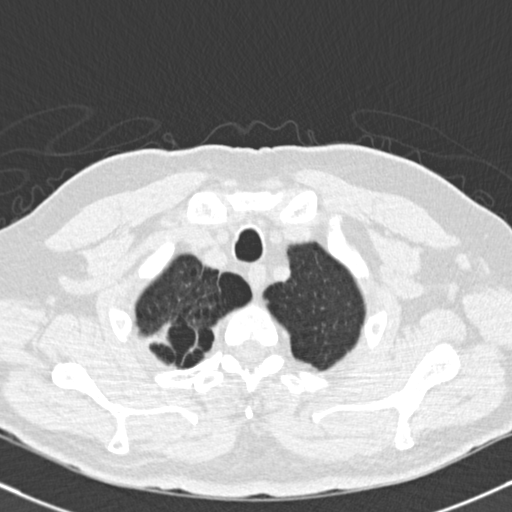
Low-dose screening chest CT, one axial slice. Slice 147 of 165 in the series (ordered by position). Reconstruction kernel B30f. Lung window (W 1500 / L -600 HU). 2 mm slice thickness. 512 × 512 image matrix.
Structures marked on this image (manually delineated by an expert):
- lesion 1 (tumor, upper lobe of right lung): bounding box (x1, y1, x2, y2) in pixels: (147, 321, 174, 346)